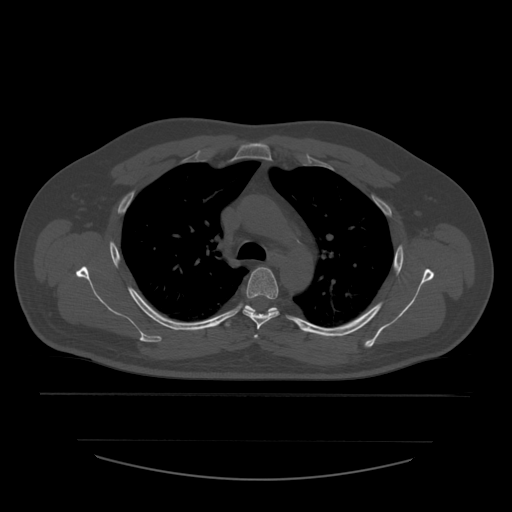
CT including the spine, one axial slice; position 413 of 532 along the scan axis; 120 kVp; bone window (W 1800 / L 400 HU); 1.25 mm slice thickness; 512 × 512 image matrix, field of view 441 × 441 mm. Patient age 44 years. From the clinical record (not read from this slice): primary cancer: soft tissue sarcoma.
Outlined on this slice (semi-automatically segmented with operator editing):
- T3 vertebra: bounding box [x1, y1, x2, y2] px = [254, 335, 258, 339]
- T4 vertebra: [243, 267, 280, 330]
- T5 vertebra: [226, 305, 278, 327]